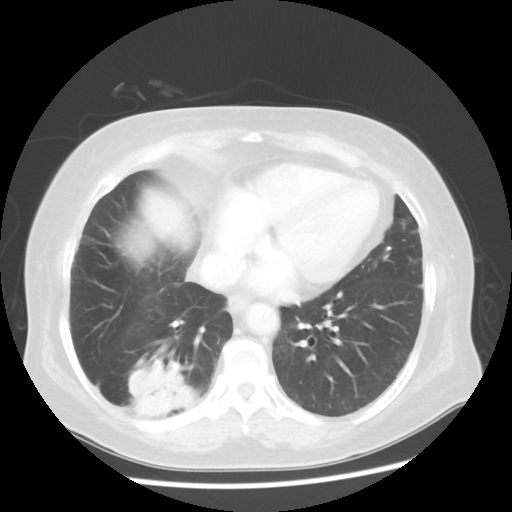
Chest CT, one axial slice. Slice 20 of 56 in the series (ordered by position). Lung window (W 1500 / L -600 HU). 512 × 512 image matrix. Female patient, age 64 years. From the clinical record (not read from this slice): clinical TNM (as recorded): Tis N0 M0.
Outlined on this slice (rectangle marked by the reading radiologist):
- lung tumour (recorded histology: adenocarcinoma): box from (x=121, y=353) to (x=202, y=433) px